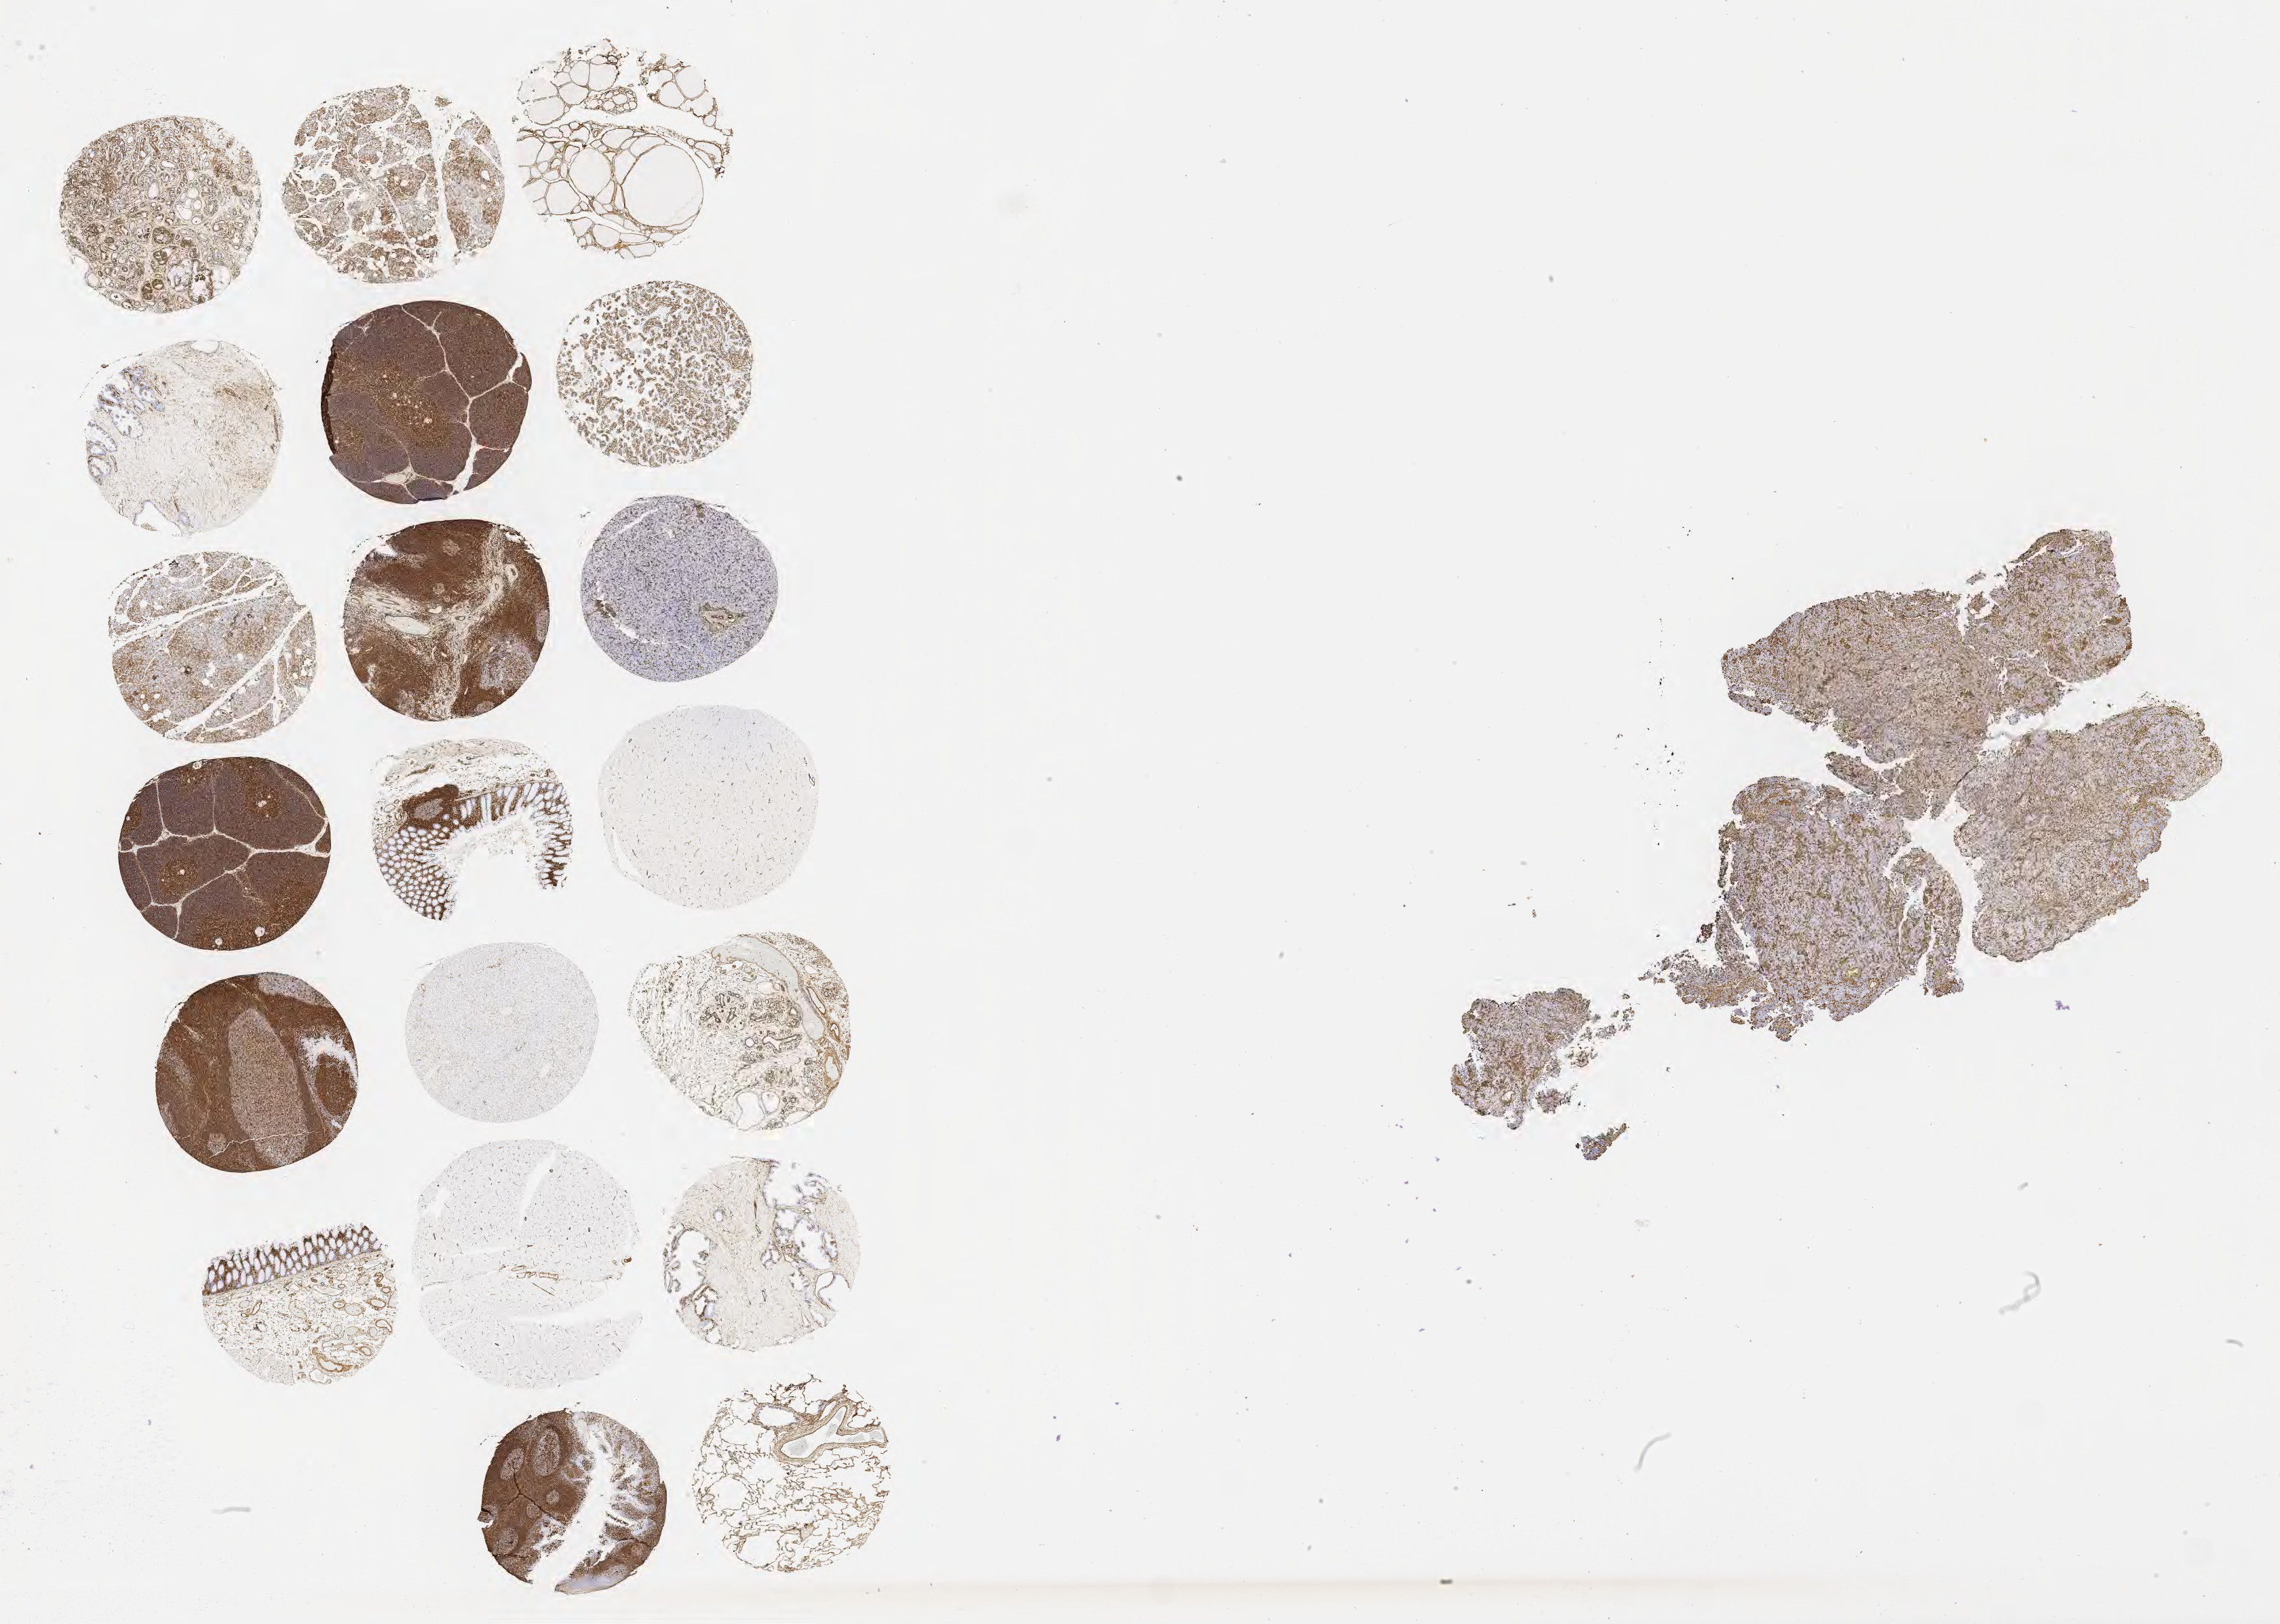
IHC for vimentin, whole-slide image, low-resolution overview of the scanned area, about 27.2 x 19.4 mm; specimen: tumor tissue; site: cervix. Patient: female, age 75 years.
Histologic diagnosis: Adenocarcinoma, NOS.